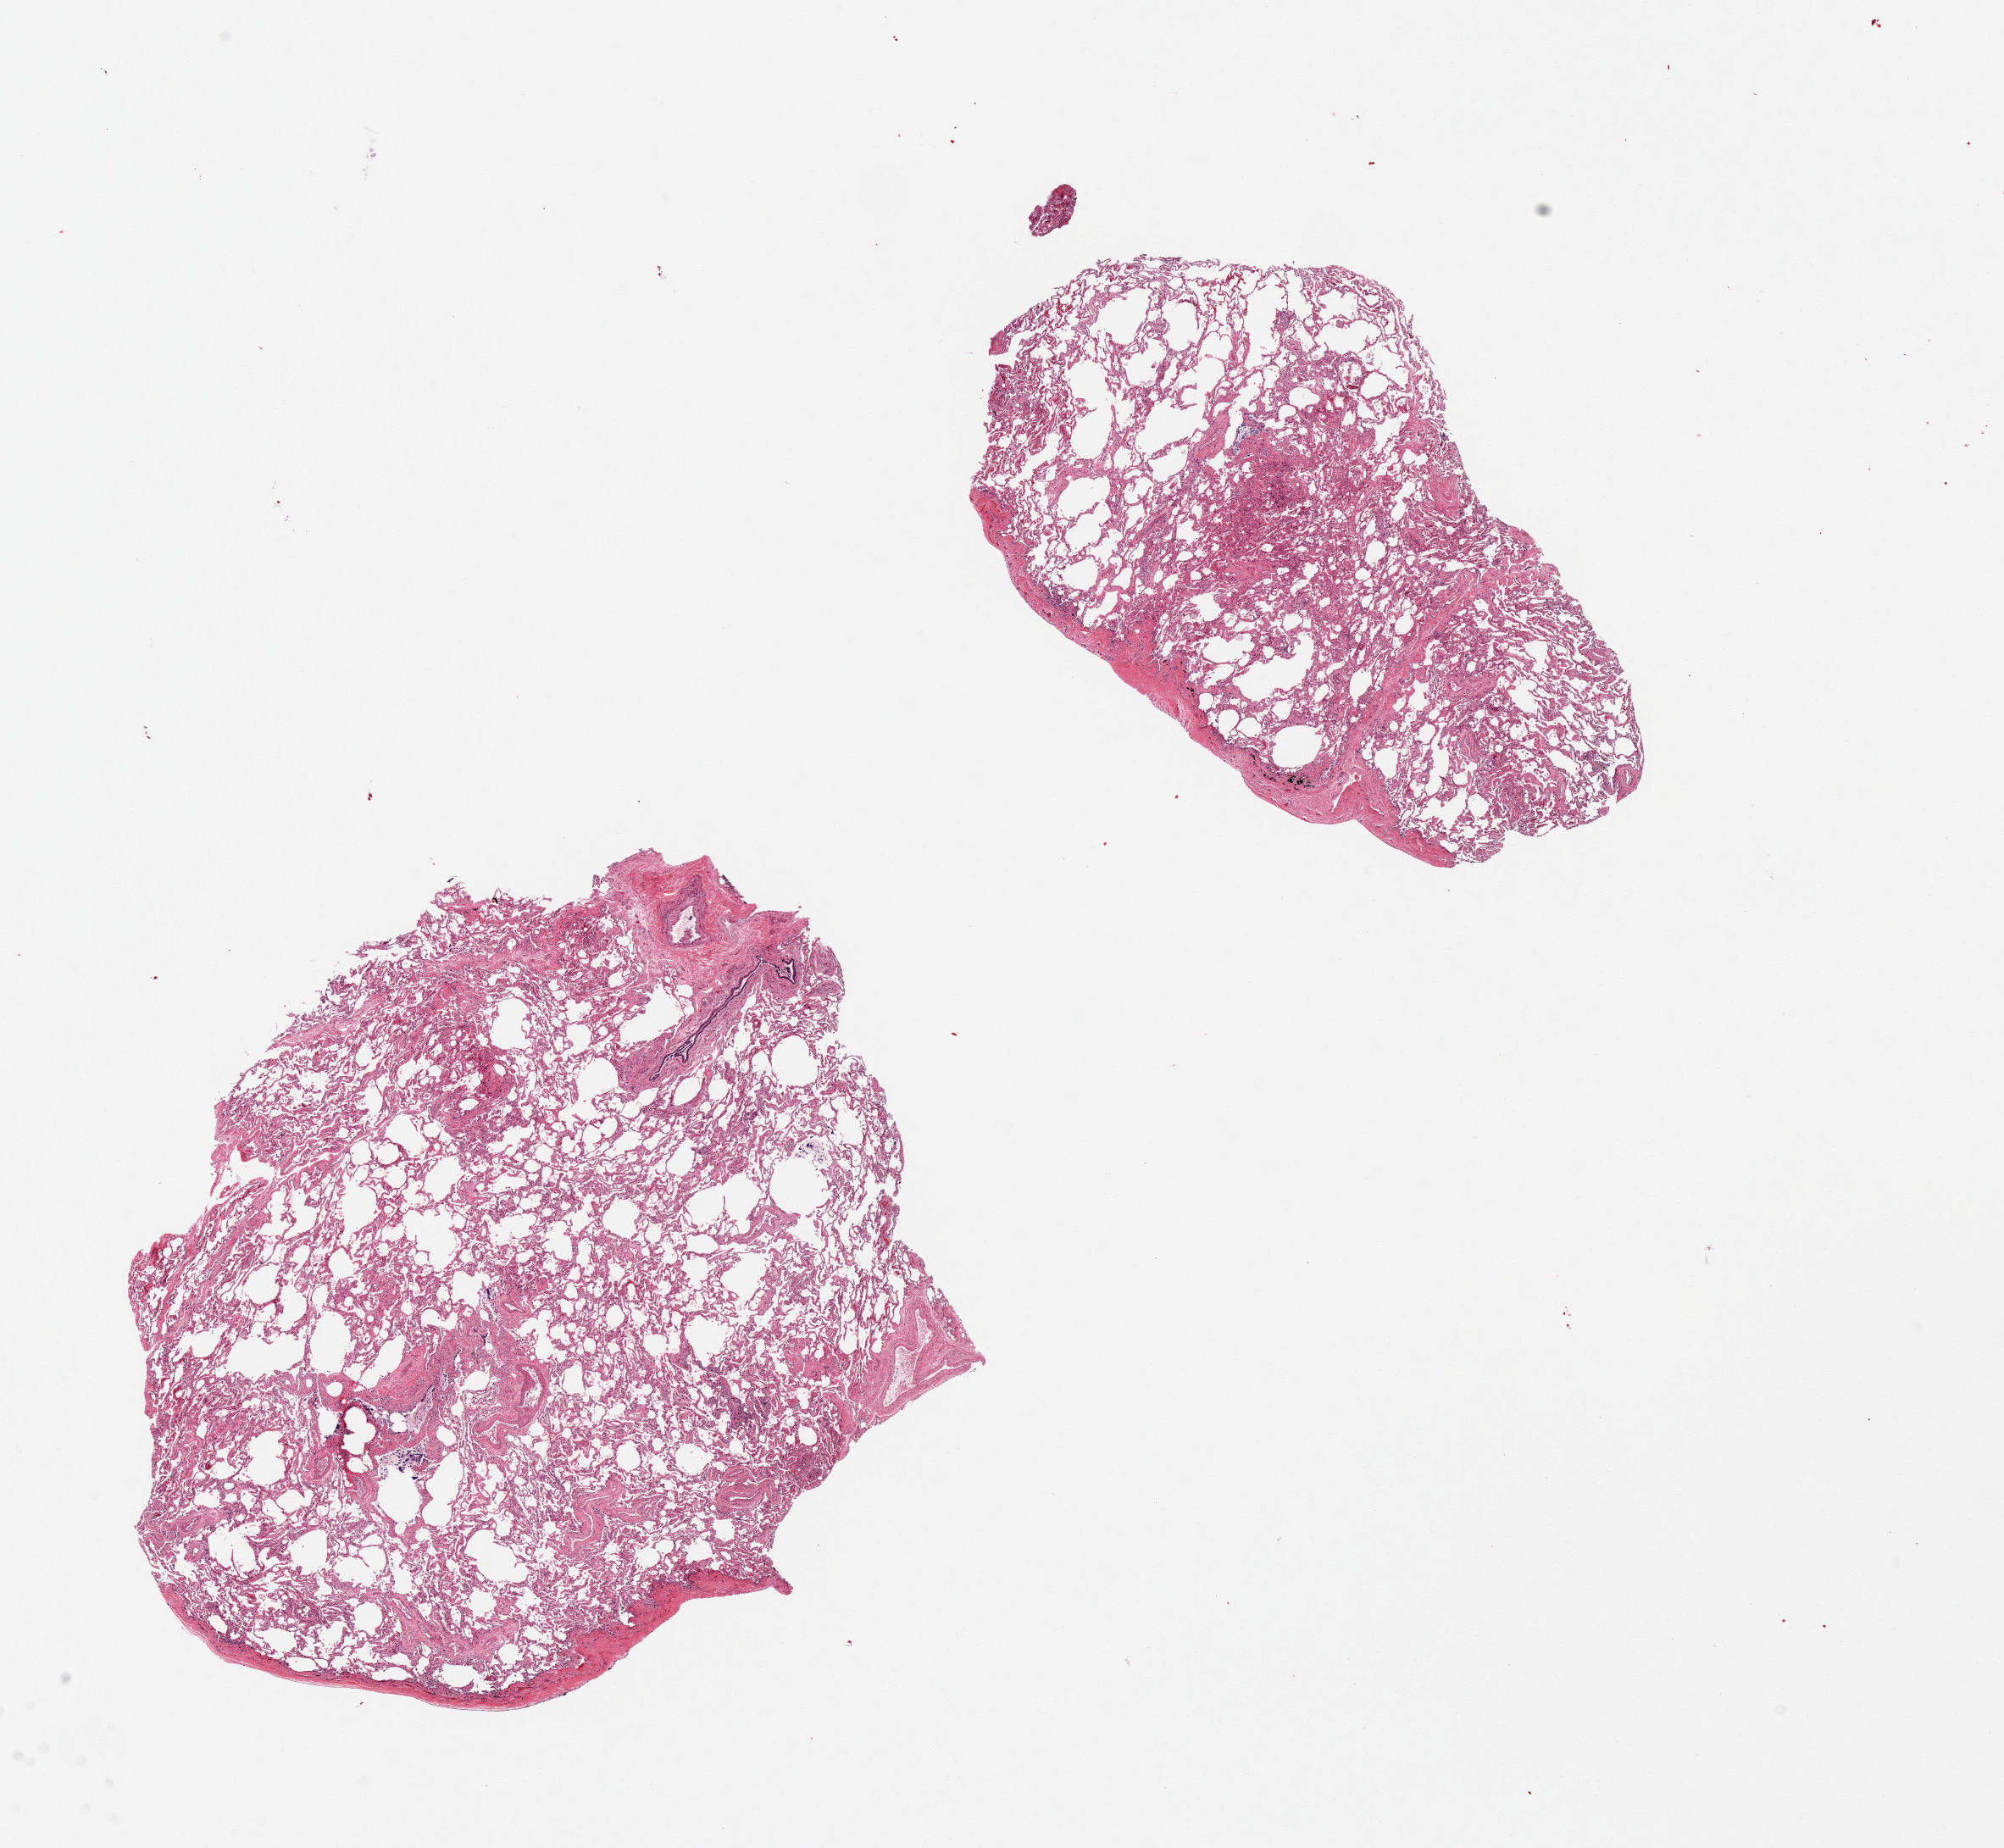
Digitized H&E-stained section, brightfield, a low-resolution overview of the entire scanned area, about 18.7 x 17.2 mm; PAXgene-fixed, paraffin-embedded tissue; section of lung (target tissue); tissue donor sample. Male donor.
• pathologist's review note for this sample: 2 pieces, moderate edema/congestion, moderately-markedly autolyzed